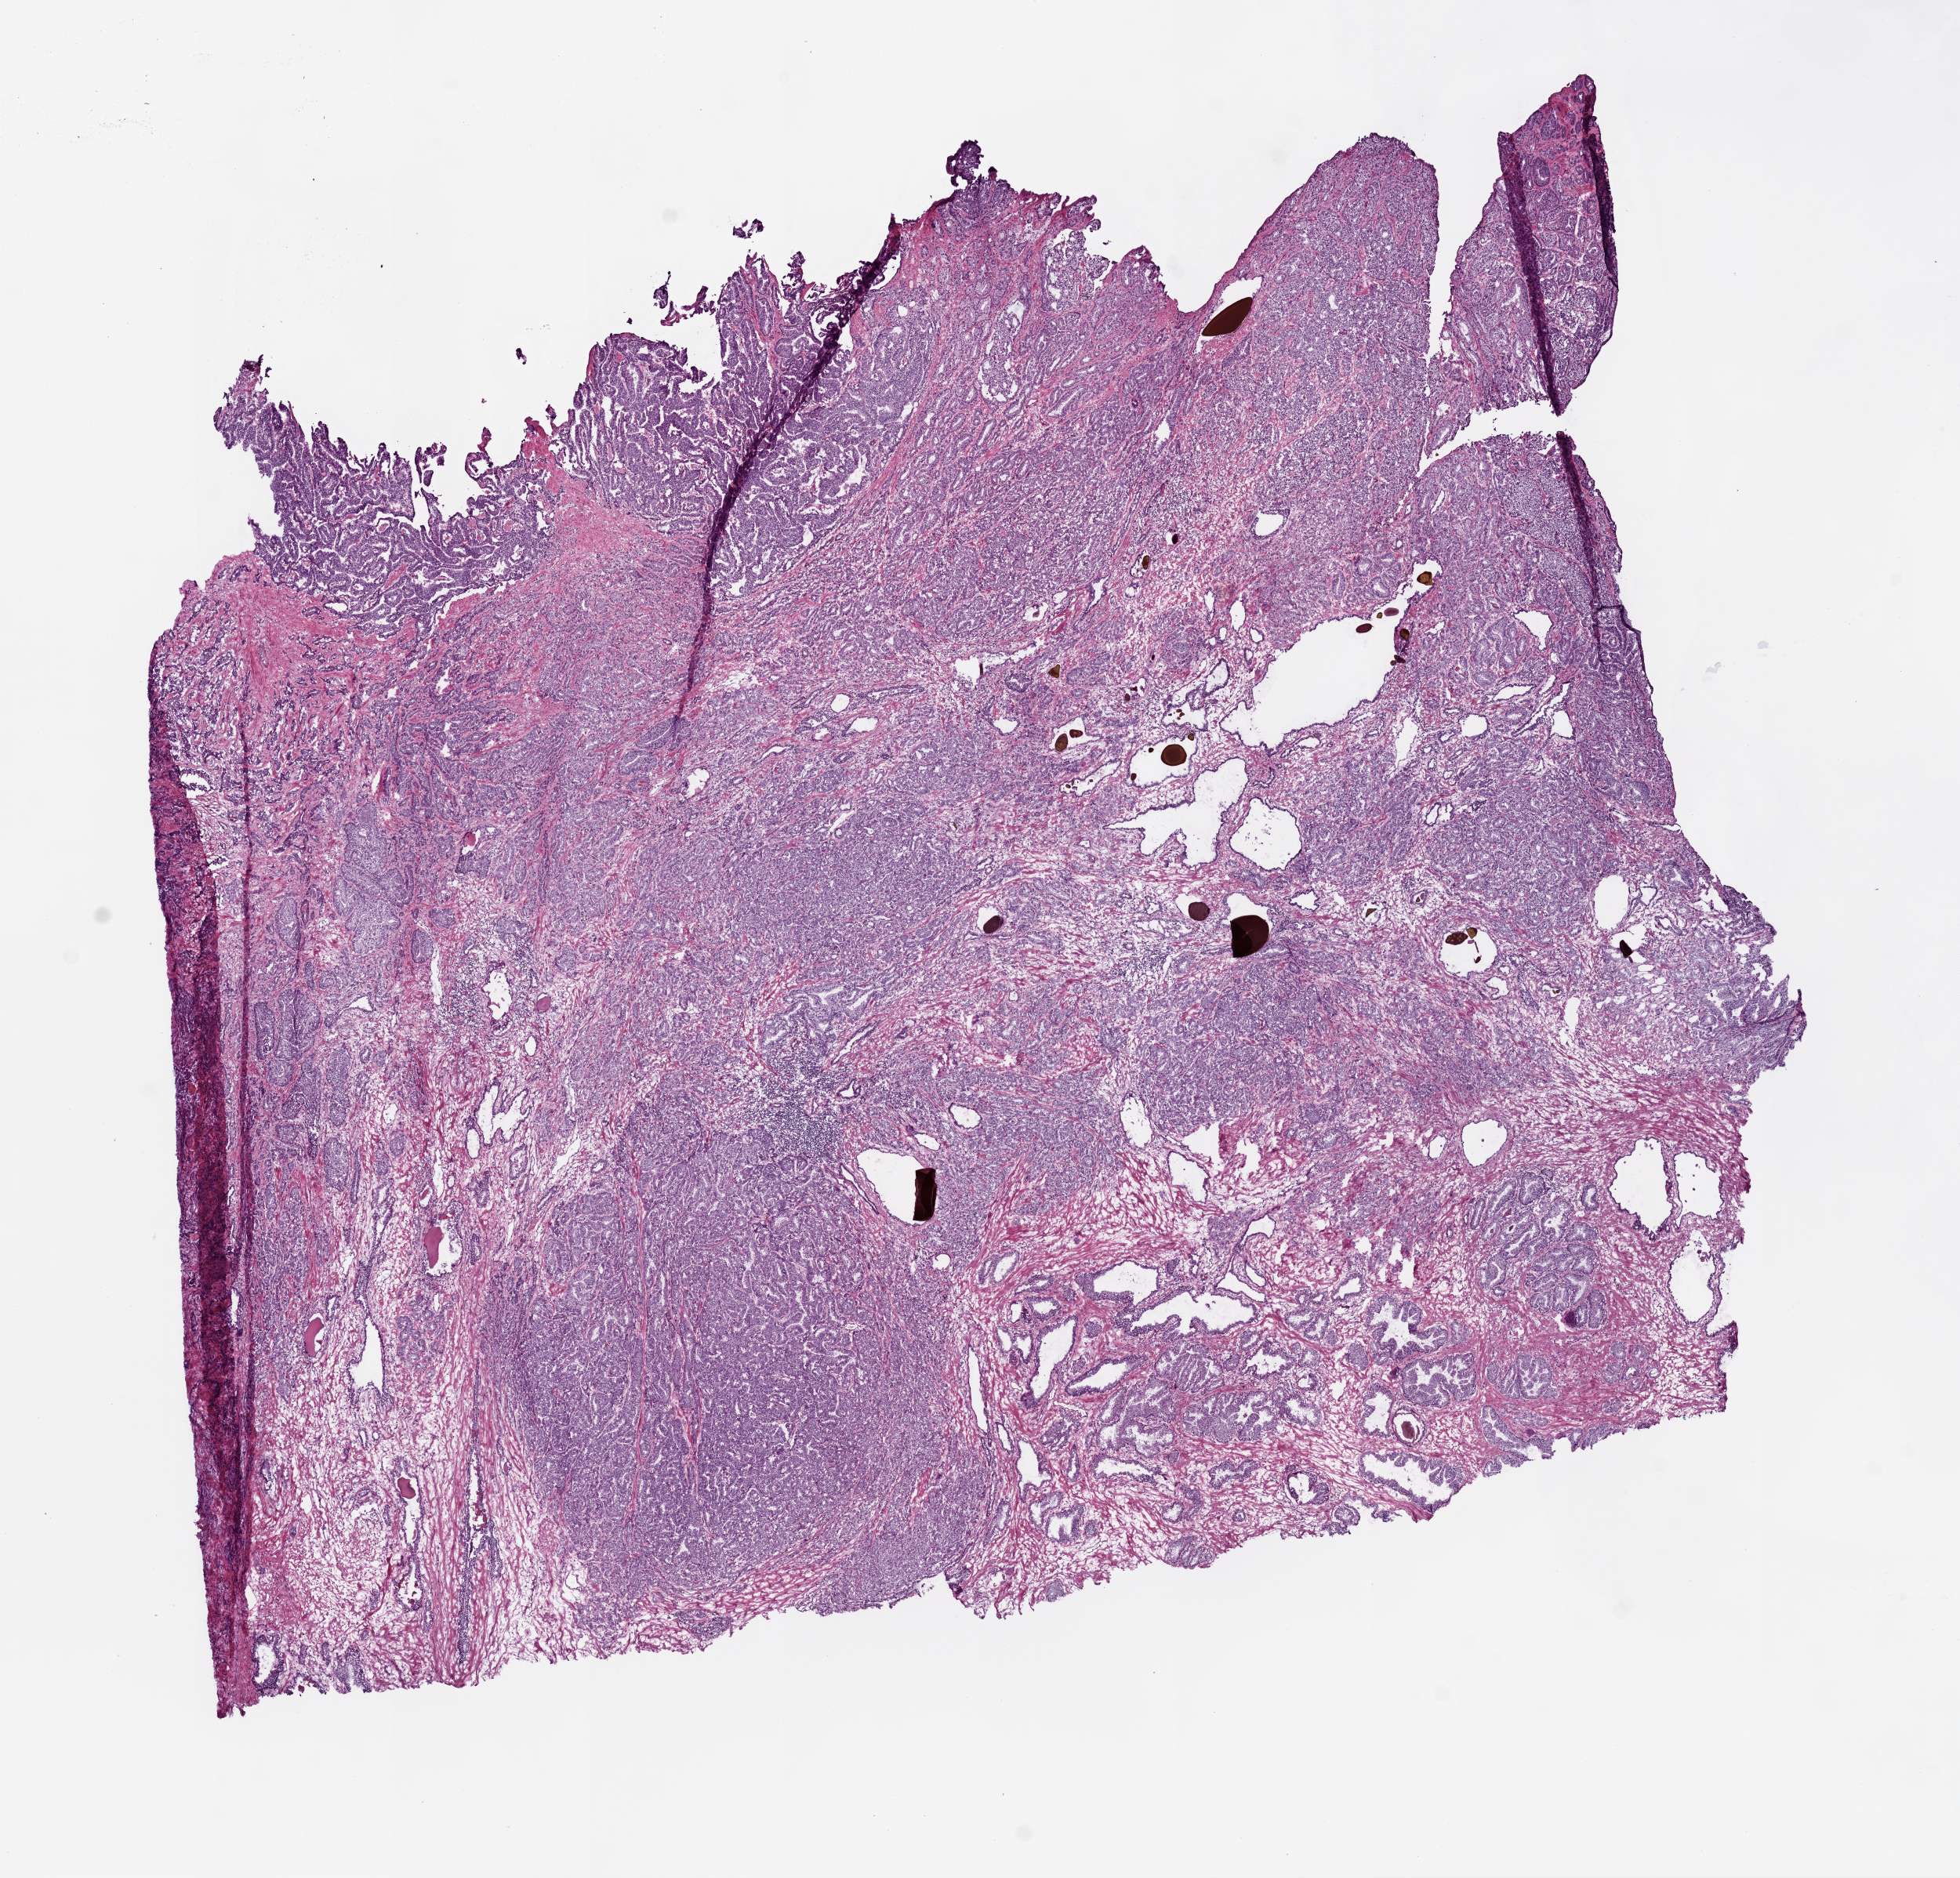
Hematoxylin and eosin (H&E) stained whole-slide image, whole scanned area (about 10.0 x 9.6 mm) shown as a low-resolution overview. Frozen section. Primary tumour sample from the prostate. Male, age 62 years at initial diagnosis. Gleason score: 7 (4+3). Composition of this section per pathologist review: tumour cells 65%, tumour nuclei 70%, normal cells 15%, stromal cells 30%, necrosis 0%. Inflammatory infiltration, as recorded: lymphocyte infiltration 4%, monocyte infiltration 2%, neutrophil infiltration 0%.
* histologic diagnosis: Acinar cell carcinoma (prostate gland)
* laterality: bilateral